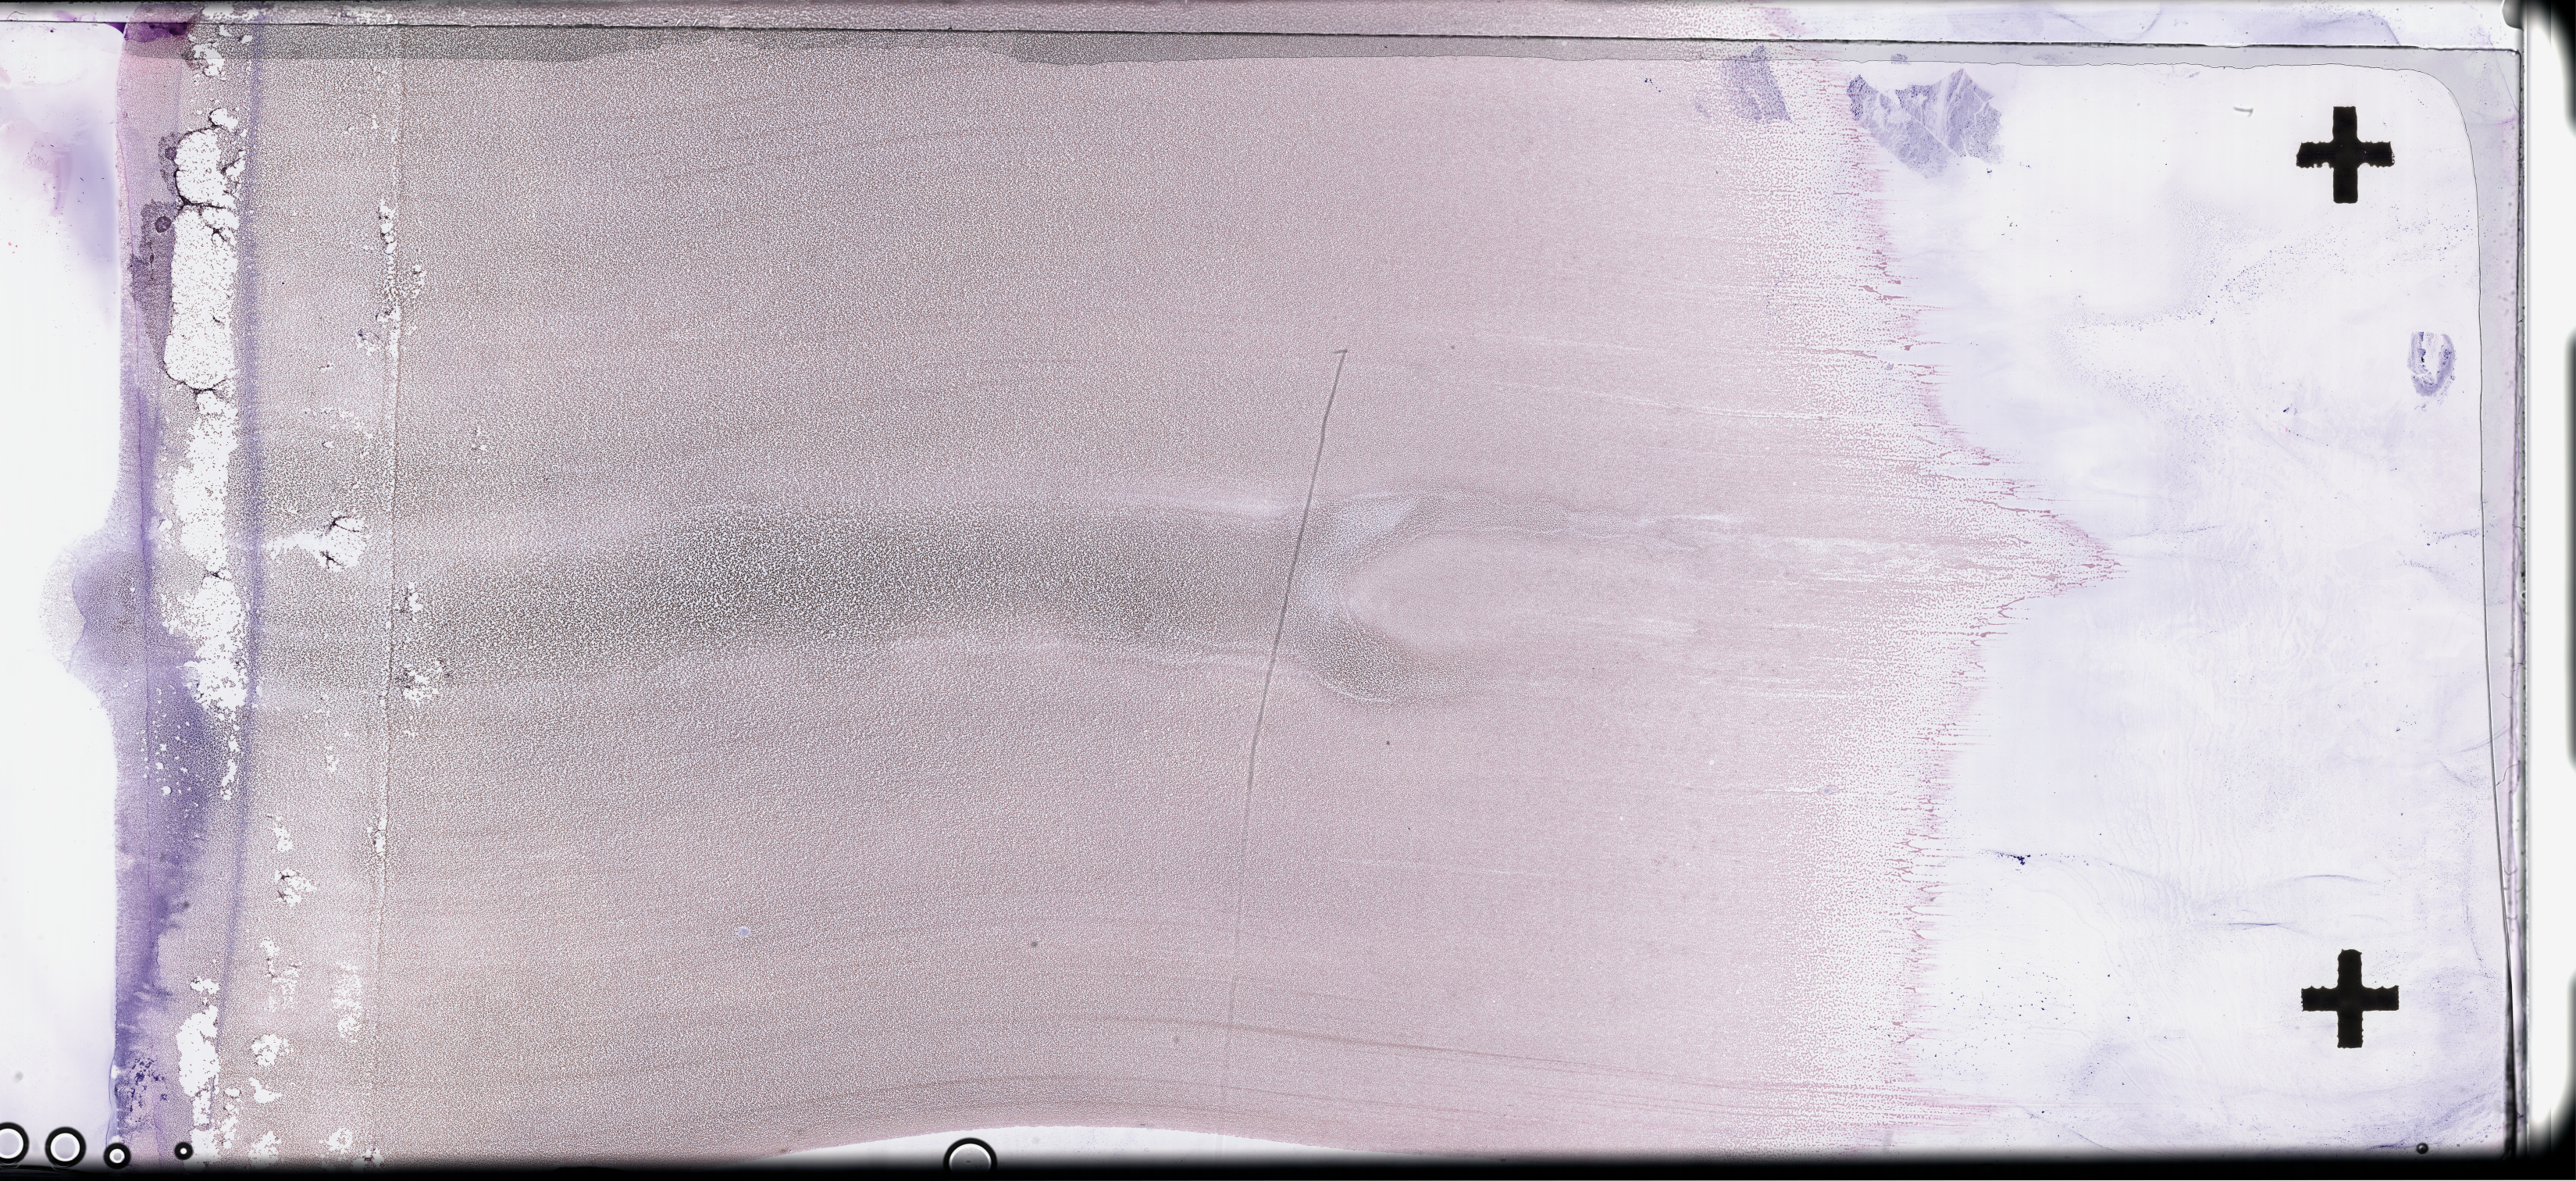
Whole-slide image of a whole blood smear, Wright-Giemsa stain — whole scanned area (about 53.3 x 24.4 mm) shown as a low-resolution overview, smear from an EDTA sample. Patient: male.
From a patient with: Plasma Cell Myeloma.